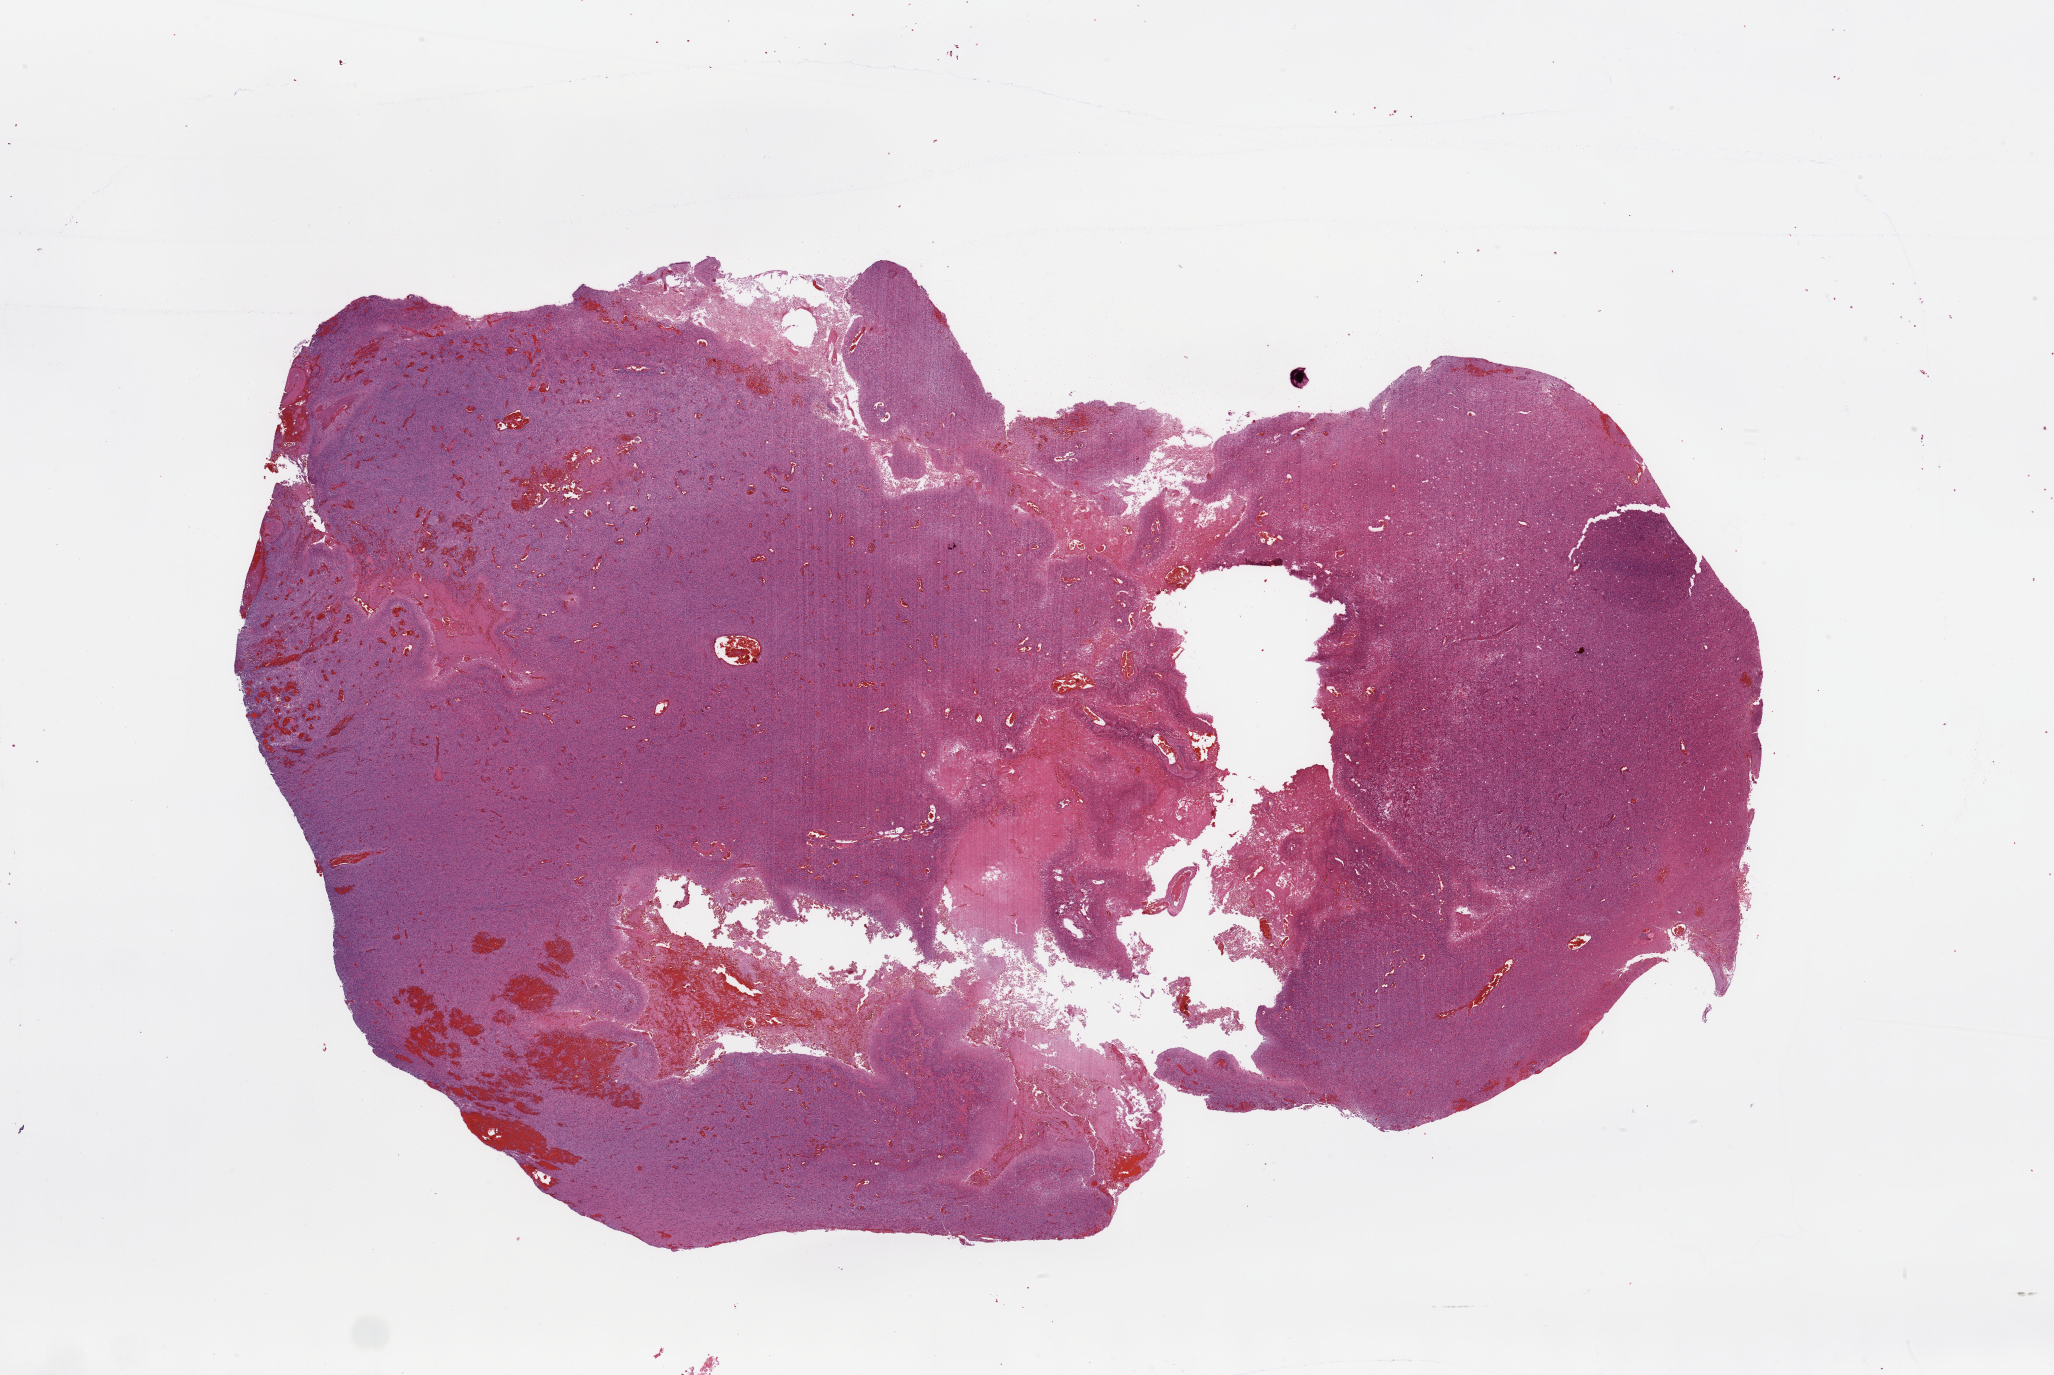
Digitized H&E-stained tissue section (whole slide), a low-resolution overview of the entire scanned area, about 32.5 x 21.7 mm (acquisition: 20x scan). Tumour tissue sample, sampled site: frontal lobe. 64-year-old female patient.
Diagnosis: Glioblastoma.